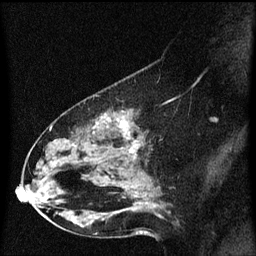
Breast MRI (dynamic contrast-enhanced), one sagittal slice; position 36 of 60 along the scan axis; dynamic contrast-enhanced series, image 2 of 3 at this slice position (ordered by acquisition); 1.5 T; TE 4.2 ms, TR 8.4 ms; 256 × 256 image matrix, field of view 200 × 200 mm. Female patient, age 49 years. From the clinical record (not read from this slice): setting: breast cancer imaged before/during neoadjuvant chemotherapy; receptor status: HR-positive, HER2-negative.
Annotated regions visible in this slice (semi-automatically segmented with operator editing):
- analysis volume of interest (the breast-tissue region the enhancement analysis was run in; not a lesion): bounding box <27,96,166,221> (left, top, right, bottom; pixels)
- tumour enhancement mask (voxels above the 70 % enhancement threshold inside the analysis volume of interest): <117,118,135,153>